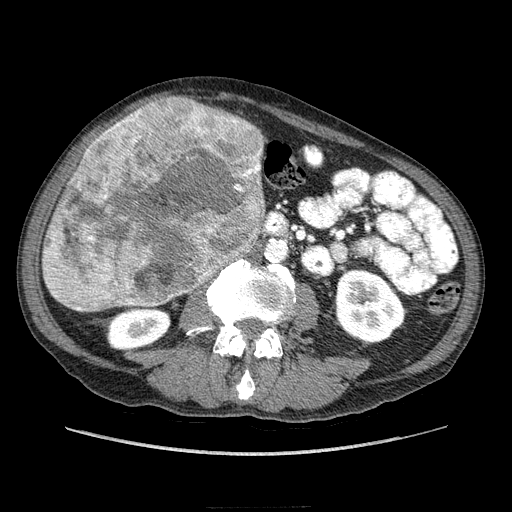
Contrast-enhanced abdominal CT (liver protocol), one axial slice. Position 71 of 218 along the scan axis. Reconstruction kernel STANDARD. 100 kVp. Soft-tissue window (W 400 / L 40 HU). 2.5 mm slice thickness. 512 × 512 image matrix, field of view 380 × 380 mm. Case-level facts recorded for this patient, not image findings: diagnosis: hepatocellular carcinoma (patient treated with transarterial chemoembolisation; whether this scan precedes or follows treatment is not stated here); TNM stage (as recorded): Stage-IIIA; Child-Pugh class: A.
Outlined on this slice (semi-automatically segmented with operator editing):
- liver parenchyma outside the tumour (the mass and vessels are separate outlines, so this box may not span the whole liver): bounding box [x1, y1, x2, y2] px = [42, 102, 197, 308]
- mass: [44, 98, 267, 311]